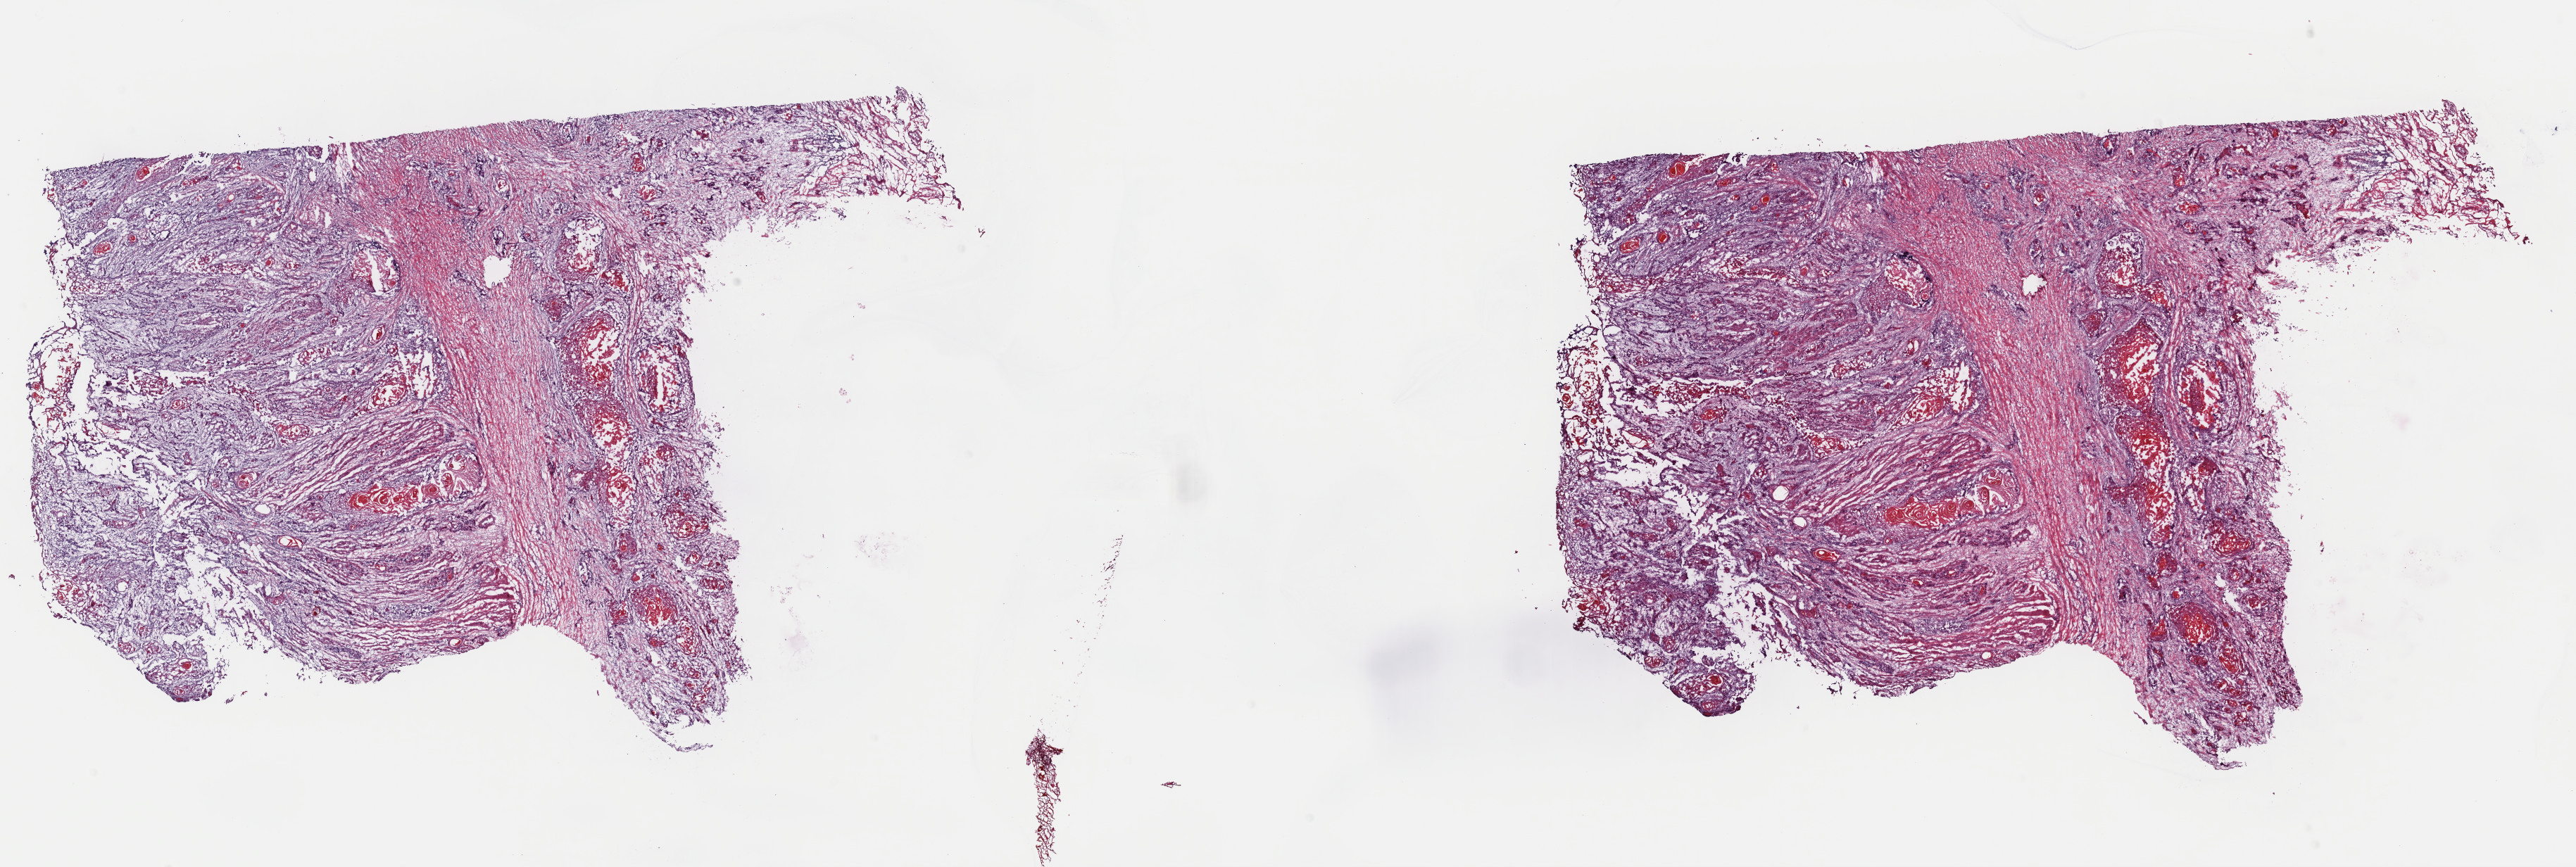
Digitized H&E tissue section (whole slide), low-resolution overview of the scanned area, about 28.9 x 9.7 mm. Frozen section. Esophagus, primary tumour sample. Male patient; age at initial diagnosis 72 years. Histologic grade: G2 (moderately differentiated). Pathologist review of this section (percent, as recorded): tumour cells 75%, tumour nuclei 75%, normal cells 0%, stromal cells 25%, necrosis 0%. Inflammatory infiltration, as recorded: lymphocyte infiltration 1%, monocyte infiltration 0%, neutrophil infiltration 0%.
Histologic diagnosis: Squamous cell carcinoma, NOS. AJCC pathologic stage: IIIA (7th edition).